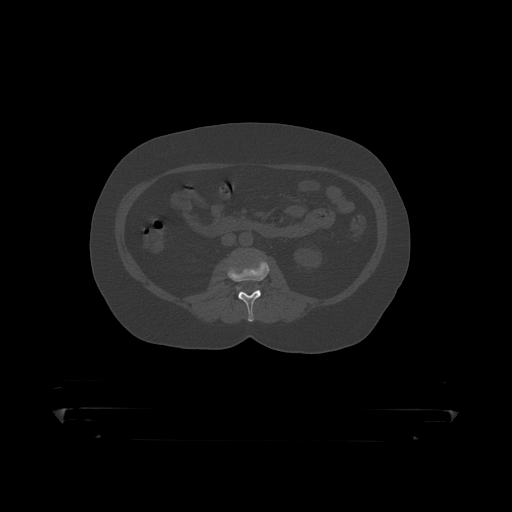
CT including the spine, one axial slice. Position 109 of 390 along the scan axis. Bone window (W 1800 / L 400 HU). 1.25 mm slice thickness. 512 × 512 image matrix, field of view 650 × 650 mm. Patient: male, 60 years. Case-level facts recorded for this patient, not image findings: primary cancer: prostate.
Outlined on this slice (semi-automatically segmented with operator editing):
- L2 vertebra: bounding box <227,254,269,319> (left, top, right, bottom; pixels)